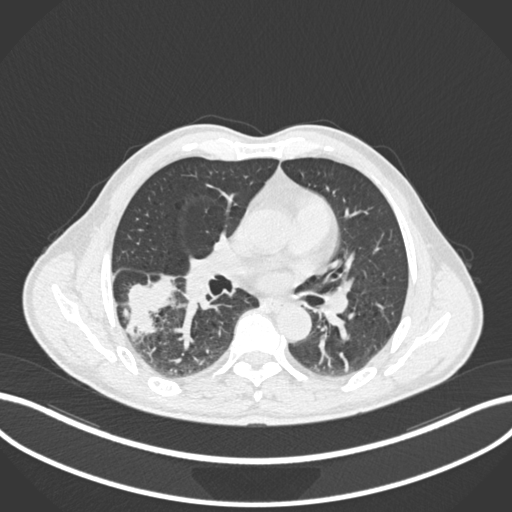
Chest CT, one axial slice. Slice 103 of 208 in the series (ordered by position). Reconstruction kernel B30f. 120 kVp. Lung window (W 1500 / L -600 HU). 1 mm slice thickness. 512 × 512 image matrix, field of view 400 × 400 mm. Male patient, age 58 years. From the clinical record (not read from this slice): clinical TNM (as recorded): T3 N0 M0; histopathological grade: G2.
Annotated regions visible in this slice (bounding box drawn by a radiologist):
- lung tumour (recorded histology: squamous cell carcinoma): bounding box <121,269,180,343> (left, top, right, bottom; pixels)